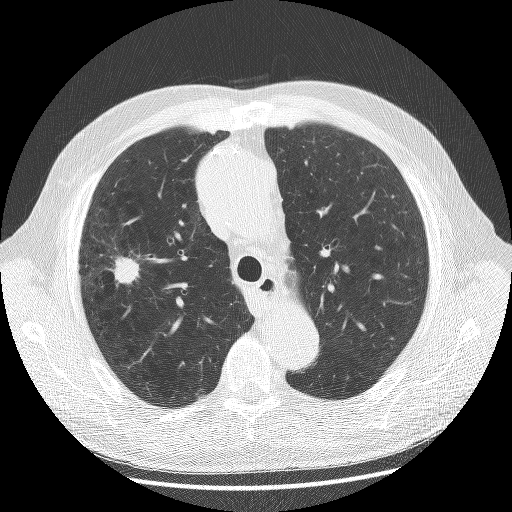
Chest CT (low-dose screening protocol), one axial image; baseline annual screen; lung window (W 1500 / L -600 HU); 2.5 mm slice thickness; lung (sharp) reconstruction kernel (BONE); slice 45 of 175 in the series; 512 × 512 image matrix, field of view 380 × 380 mm. Male, age 70 years at enrolment. Current smoker at enrolment.
Expert reader's lesion annotation, bounding box (x1, y1, x2, y2) in pixels: (75, 238, 148, 307). The screening reader recorded 2 non-calcified nodules or masses ≥4 mm on this exam (left upper lobe, right upper lobe); which of them this box marks is not recorded. Lung cancer was diagnosed 23 days after this screen: non-small cell carcinoma, right upper lobe, poorly differentiated (G3), stage IA (AJCC 6th edition), 20 mm at pathology.